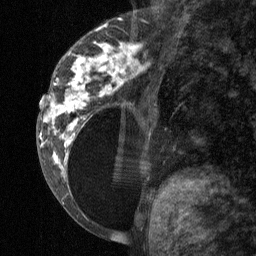
Breast MRI (dynamic contrast-enhanced), one sagittal slice; position 24 of 64 along the scan axis; dynamic contrast-enhanced study with each time point stored as its own series, time point 2 of 3 at this slice position (early post-contrast, ordered by acquisition time); 1.5 T; TE 4.8 ms, TR 27 ms; 256 × 256 image matrix, field of view 180 × 180 mm. Female patient, age 34 years. From the clinical record (not read from this slice): setting: breast cancer imaged before/during neoadjuvant chemotherapy; receptor status: HR-positive, HER2-negative.
Outlined on this slice (semi-automatic segmentation, software-assisted and operator-edited):
- analysis volume of interest (the breast-tissue region the enhancement analysis was run in; not a lesion): box from (x=41, y=23) to (x=157, y=197) px
- tumour enhancement mask (voxels above the 90 % enhancement threshold inside the analysis volume of interest): (x=41, y=42)–(x=146, y=176)